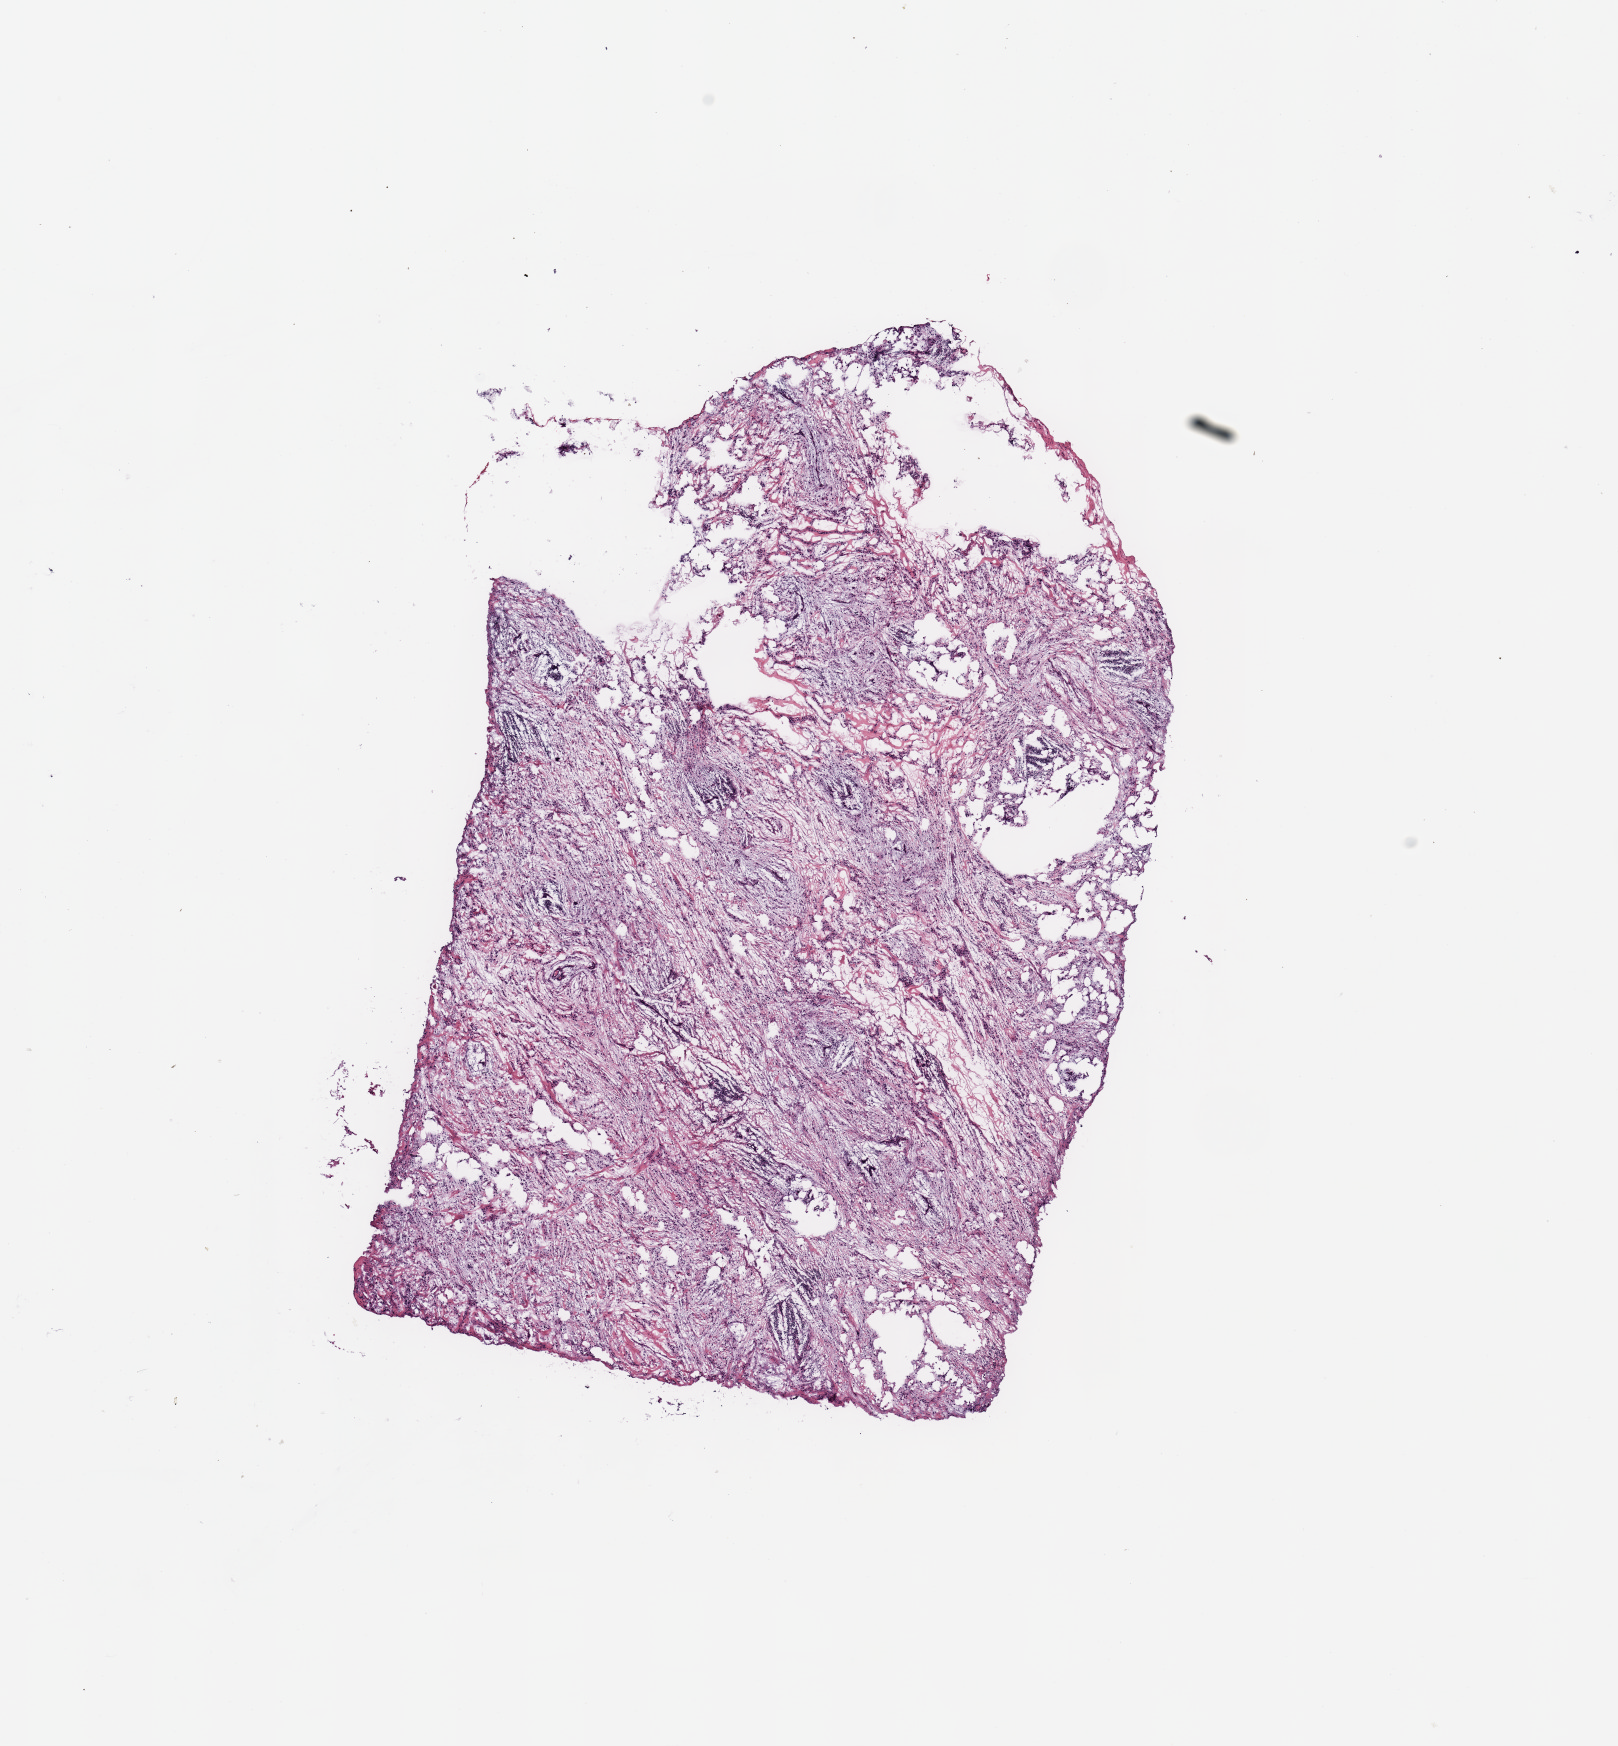
H&E whole-slide image, whole scanned area (about 12.8 x 13.8 mm, from a 20x scan) shown as a low-resolution overview, breast, tissue type not recorded.
Patient diagnosis (cohort enrolment): breast cancer (breast).